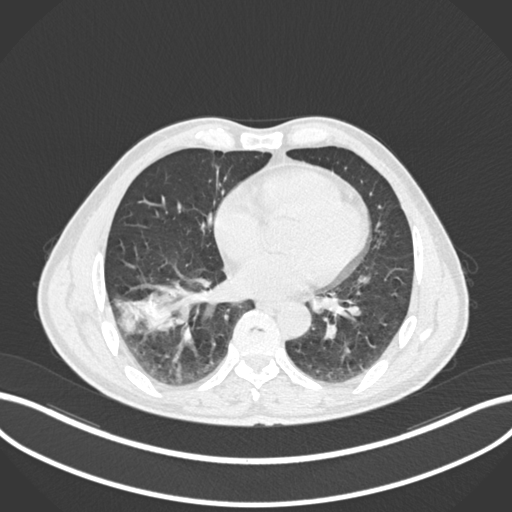
Chest CT, one axial slice; lung window (W 1500 / L -600 HU); 1 mm slice thickness; 512 × 512 image matrix, field of view 400 × 400 mm. Male patient, age 58 years. From the clinical record (not read from this slice): clinical TNM (as recorded): T3 N0 M0.
Outlined on this slice (rectangle marked by the reading radiologist):
- lung tumour (recorded histology: squamous cell carcinoma): box from (x=104, y=283) to (x=190, y=343) px